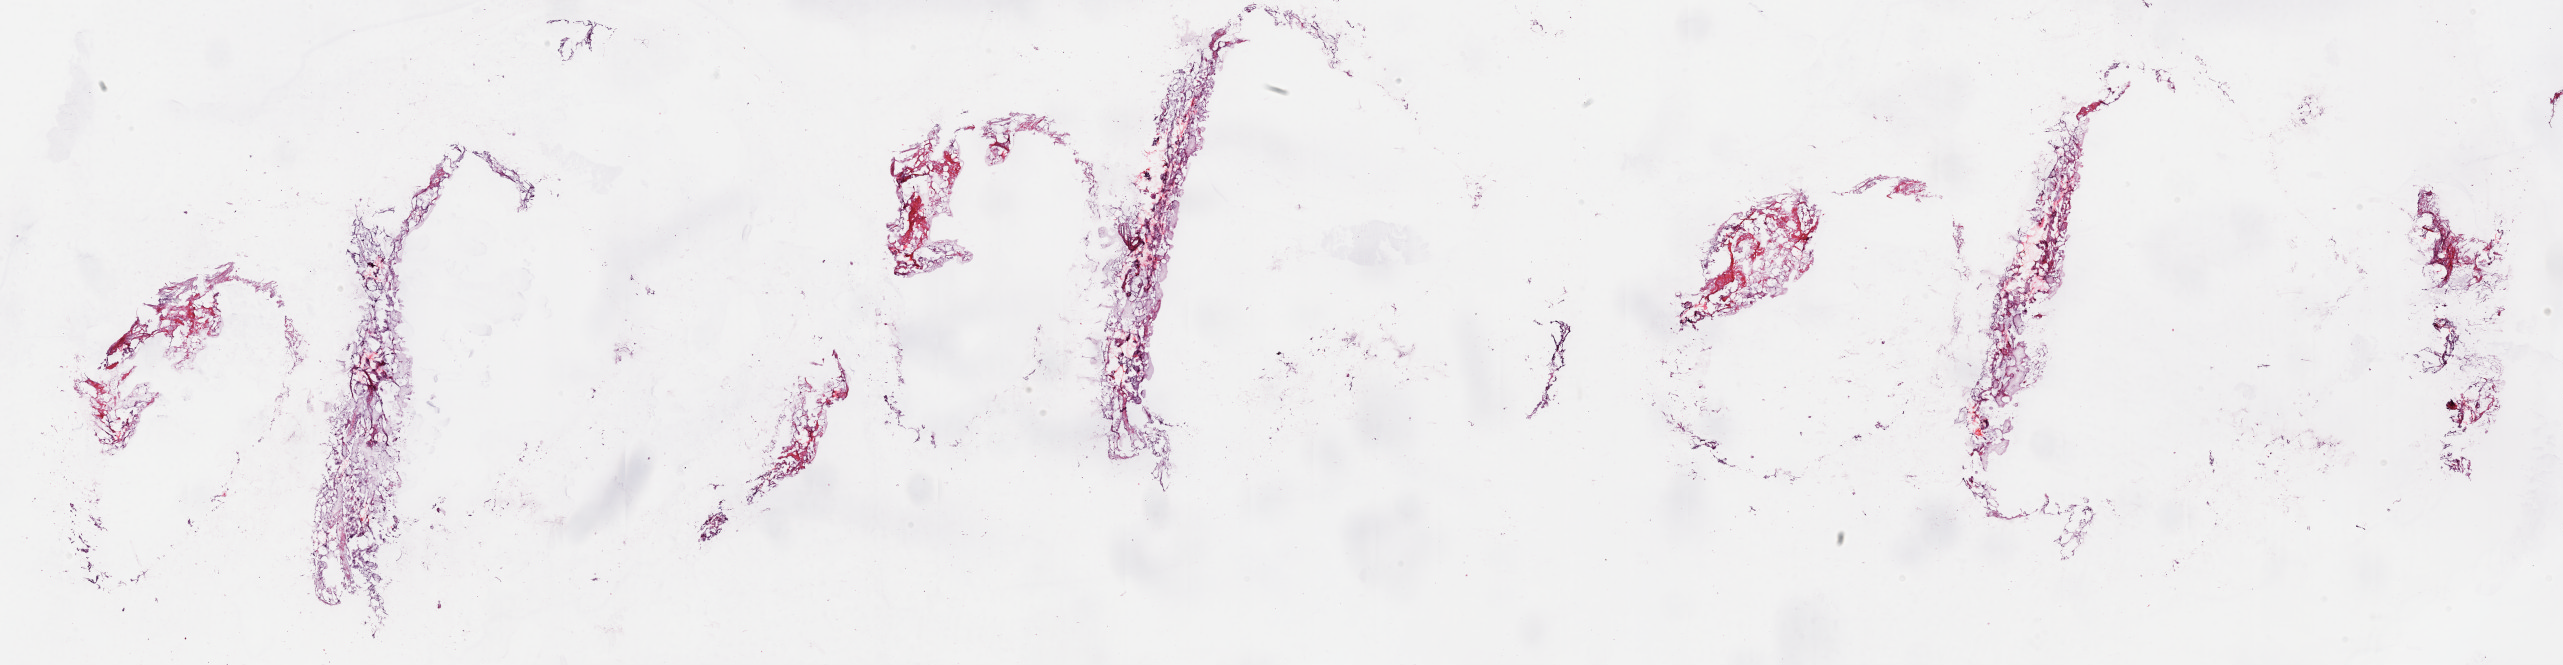
H&E whole-slide image — shown as a low-resolution overview of the whole scanned area (about 40.7 x 10.6 mm). Frozen section. Solid tissue normal (non-tumour tissue) sample from the breast. Female patient; age at initial diagnosis 79 years. Pathologist review of this section (percent, as recorded): tumour cells 0%, normal cells 100%.
This section: solid tissue normal (non-tumour) sample from the same patient. Patient diagnosis: Infiltrating duct carcinoma, NOS.